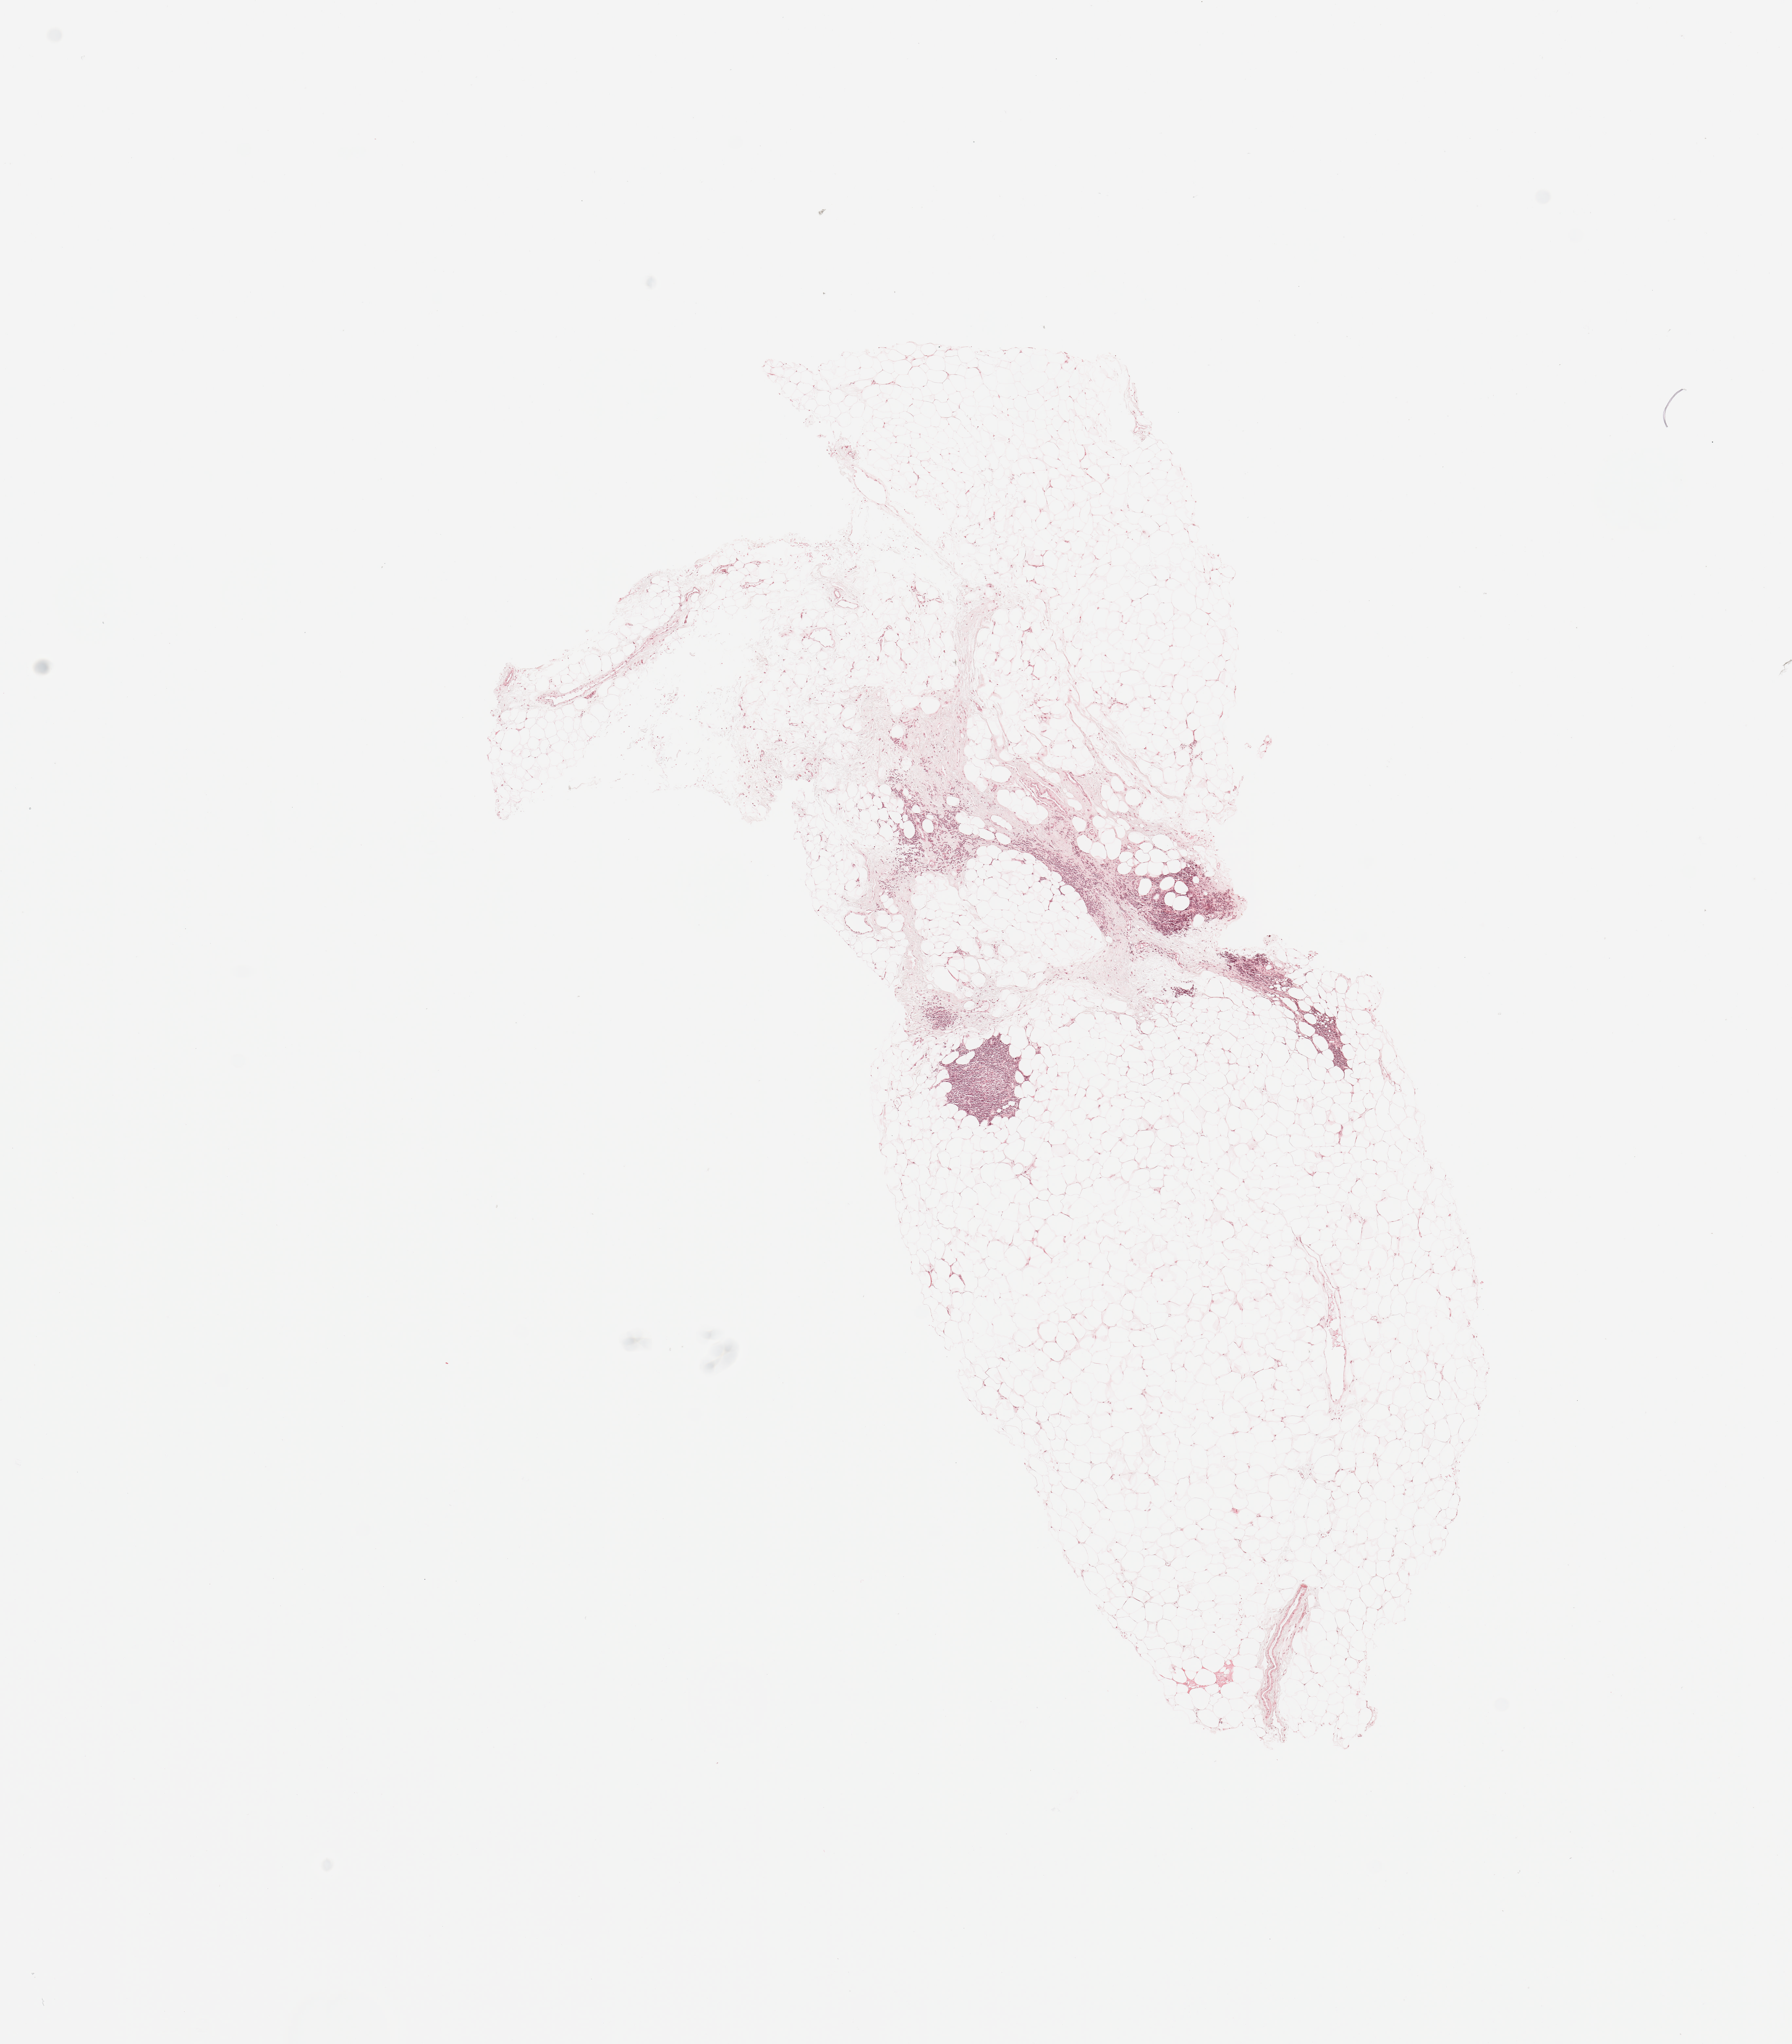
H&E whole-slide image, whole scanned area (about 10.8 x 12.4 mm) shown as a low-resolution overview; normal (non-tumour) tissue sample, kidney. 67-year-old male patient.
* this section: normal (non-tumour) tissue from the same patient
* patient diagnosis: Renal cell carcinoma, NOS